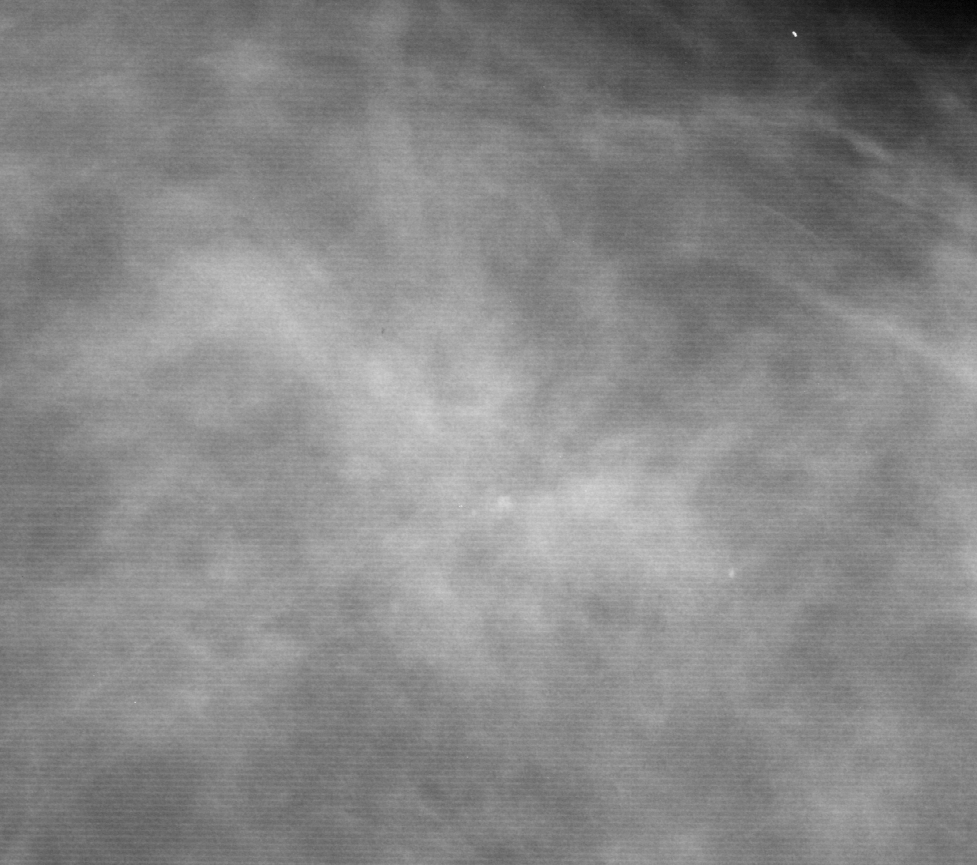
Cropped region of a digitized screen-film mammogram centred on a radiologist-marked abnormality, left breast, CC view, BI-RADS breast density category 2 (scale 1–4).
- Marked abnormality: calcifications, morphology pleomorphic, distribution clustered; BI-RADS assessment category 4; subtlety rating 4 on a 1 (subtle) to 5 (obvious) scale; pathology (as recorded): malignant.